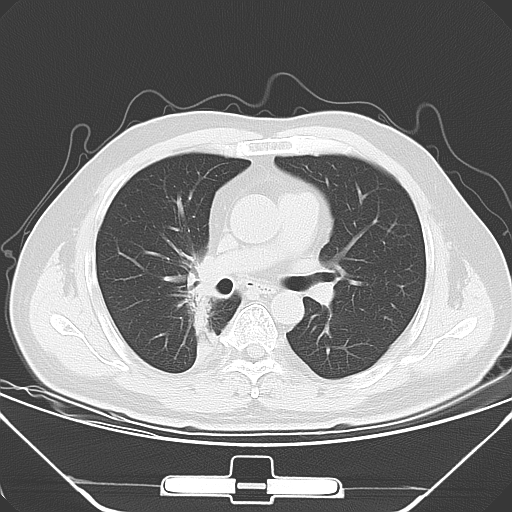
Chest CT, one axial slice; slice 31 of 56 in the series (ordered by position); 120 kVp; lung window (W 1500 / L -600 HU); 512 × 512 image matrix, field of view 371 × 371 mm. Male patient, age 48 years. From the clinical record (not read from this slice): clinical TNM (as recorded): T1a N1 M1c; histopathological grade: G3.
Annotated regions visible in this slice (bounding box drawn by a radiologist):
- lung tumour (recorded histology: adenocarcinoma): bounding box (x1, y1, x2, y2) in pixels: (178, 250, 216, 359)